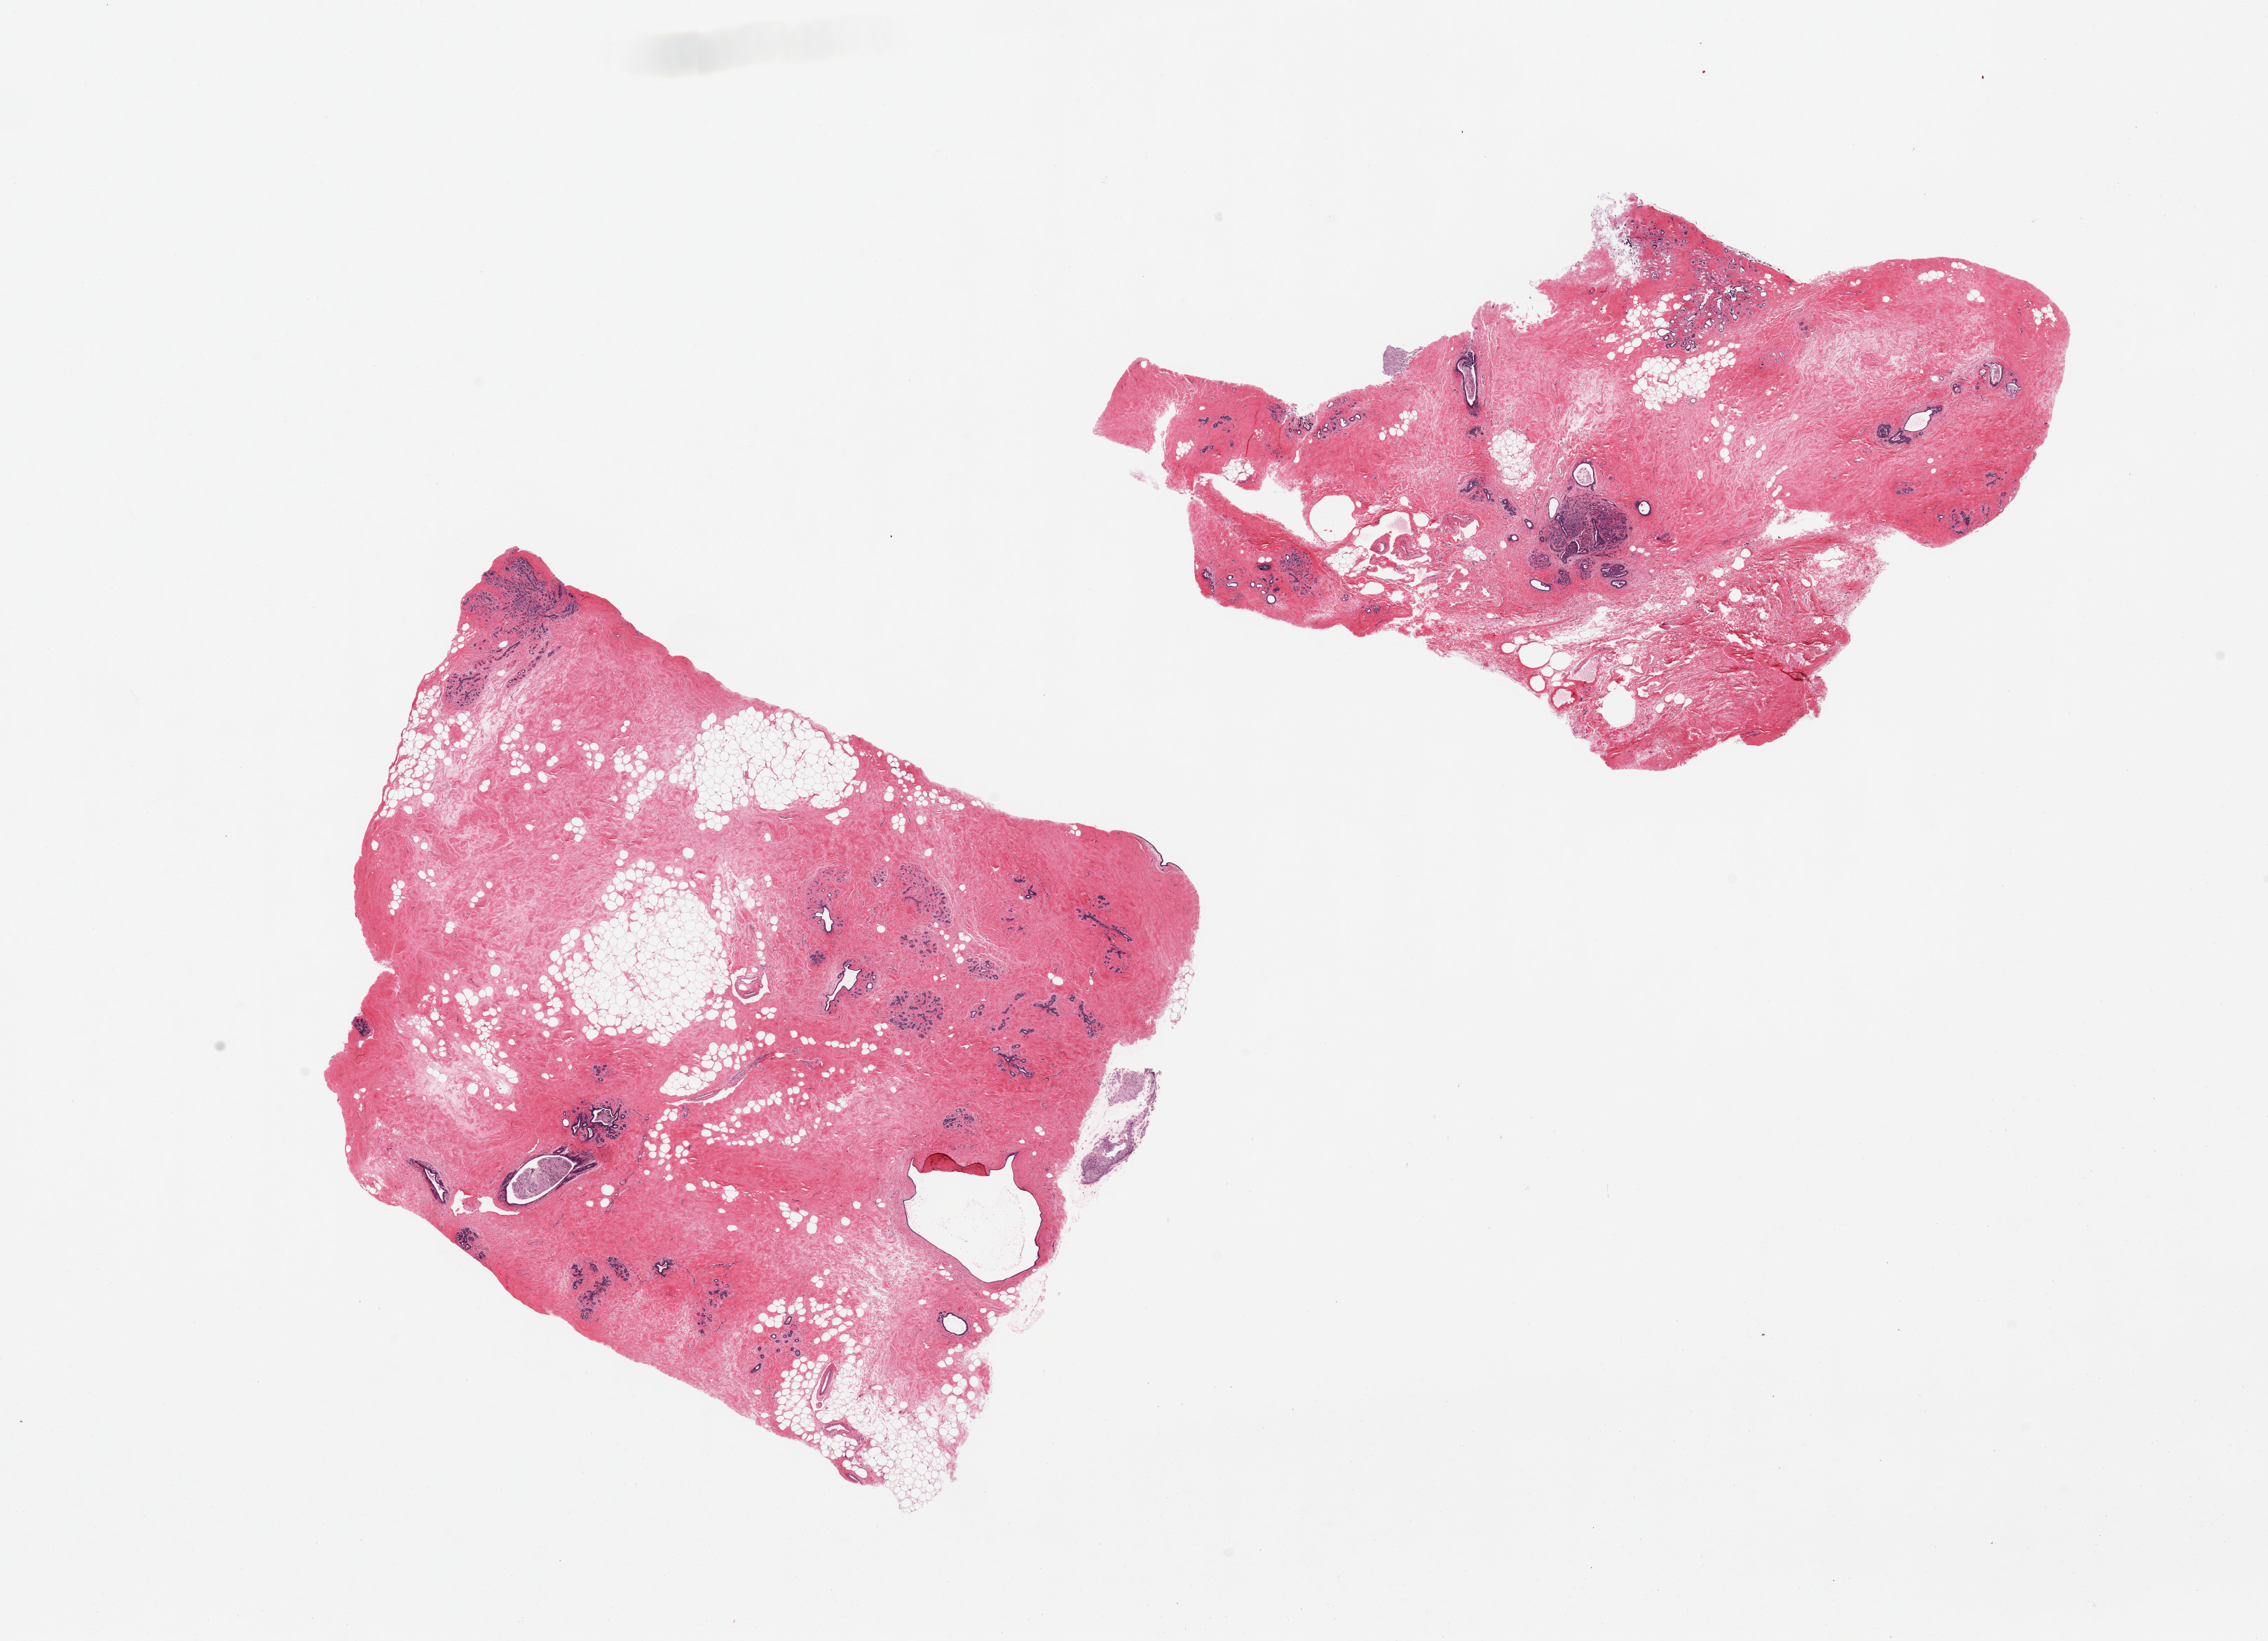
Digitized H&E-stained section, brightfield, whole scanned area (about 25.6 x 18.5 mm) shown as a low-resolution overview; PAXgene-fixed paraffin-embedded (PFPE) section; section of breast (target tissue); tissue donor sample. Female donor.
• pathologist's review note for this sample: 2 pieces, generalized fibrocystic changes